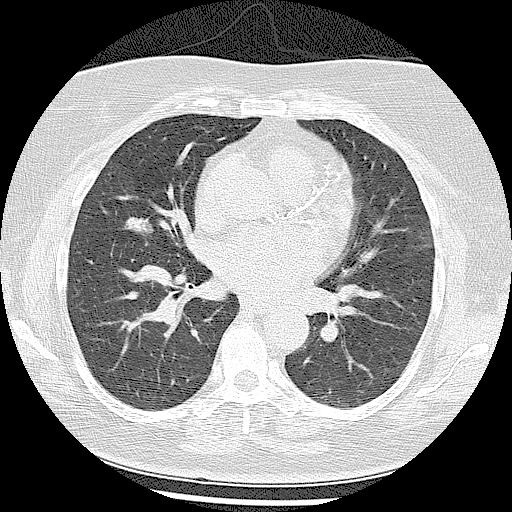
Low-dose screening chest CT, one axial slice. Reconstruction kernel LUNG. 120 kVp. Lung window (W 1500 / L -600 HU). 2.5 mm slice thickness. 512 × 512 image matrix, field of view 350 × 350 mm.
Annotated regions visible in this slice (manually delineated by an expert):
- lesion 1 (tumor, middle lobe of right lung): bounding box (x1, y1, x2, y2) in pixels: (123, 217, 154, 234)